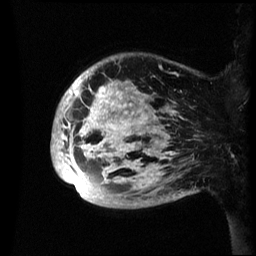
Breast MRI (dynamic contrast-enhanced), one sagittal slice; position 10 of 60 along the scan axis; dynamic contrast-enhanced series, image 2 of 3 at this slice position (ordered by acquisition); 1.5 T; TE 4.2 ms, TR 8.4 ms; 2.4 mm slice thickness; 256 × 256 image matrix. Patient: female, 48 years.
Outlined on this slice (semi-automatically segmented with operator editing):
- analysis volume of interest (the breast-tissue region the enhancement analysis was run in; not a lesion): bounding box (x1, y1, x2, y2) in pixels: (51, 54, 194, 209)
- tumour enhancement mask (voxels above the 70 % enhancement threshold inside the analysis volume of interest): (51, 80, 182, 190)